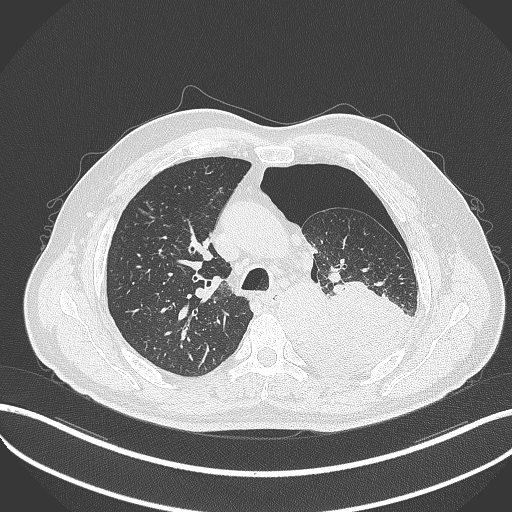
Chest CT, one axial slice. Slice 356 of 464 in the series (ordered by position). Reconstruction kernel B70f. 120 kVp. Lung window (W 1500 / L -600 HU). 512 × 512 image matrix, field of view 400 × 400 mm. Male patient, age 76 years. Case-level facts recorded for this patient, not image findings: clinical TNM (as recorded): T3 N0 M1b.
Annotated regions visible in this slice (bounding box drawn by a radiologist):
- lung tumour (recorded histology: adenocarcinoma): bounding box (x1, y1, x2, y2) in pixels: (290, 282, 413, 379)